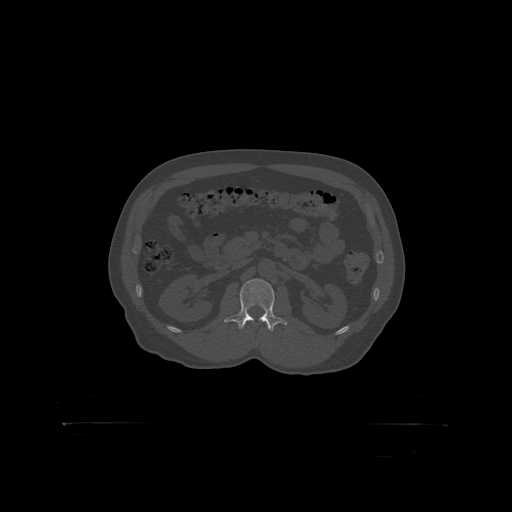
CT including the spine, one axial slice. Slice 301 of 399 in the series (ordered by position). Reconstruction kernel STANDARD. Bone window (W 1800 / L 400 HU). 1.25 mm slice thickness. 512 × 512 image matrix. Patient: male, 46 years. Case-level facts recorded for this patient, not image findings: primary cancer: skin.
Annotated regions visible in this slice (semi-automatic segmentation, software-assisted and operator-edited):
- L2 vertebra: bounding box [x1, y1, x2, y2] px = [237, 279, 275, 319]